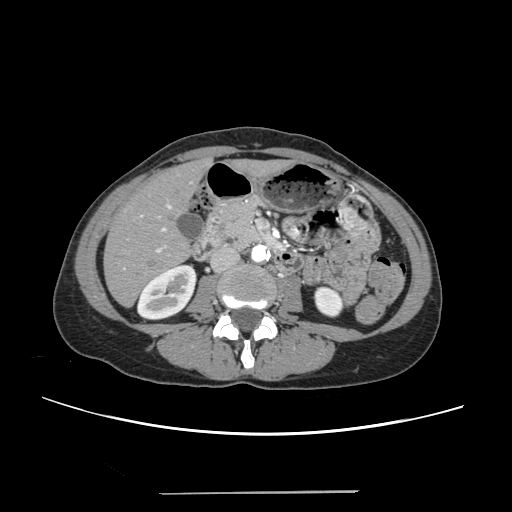
Contrast-enhanced abdominal CT, one axial slice. Position 86 of 240 along the scan axis. Intravenous contrast given. Soft-tissue window (W 400 / L 40 HU). 1.25 mm slice thickness. 512 × 512 image matrix. Female patient, age 60 years. From the clinical record (not read from this slice): diagnosis: colorectal cancer liver metastases, imaged before liver resection; multiple liver metastases: no.
Annotated regions visible in this slice (expert manual segmentation):
- liver: bounding box <105,163,280,305> (left, top, right, bottom; pixels)
- planned liver remnant (the part of the liver to remain after resection): <105,164,278,305>
- portal vein (with intrahepatic branches): <123,204,171,269>